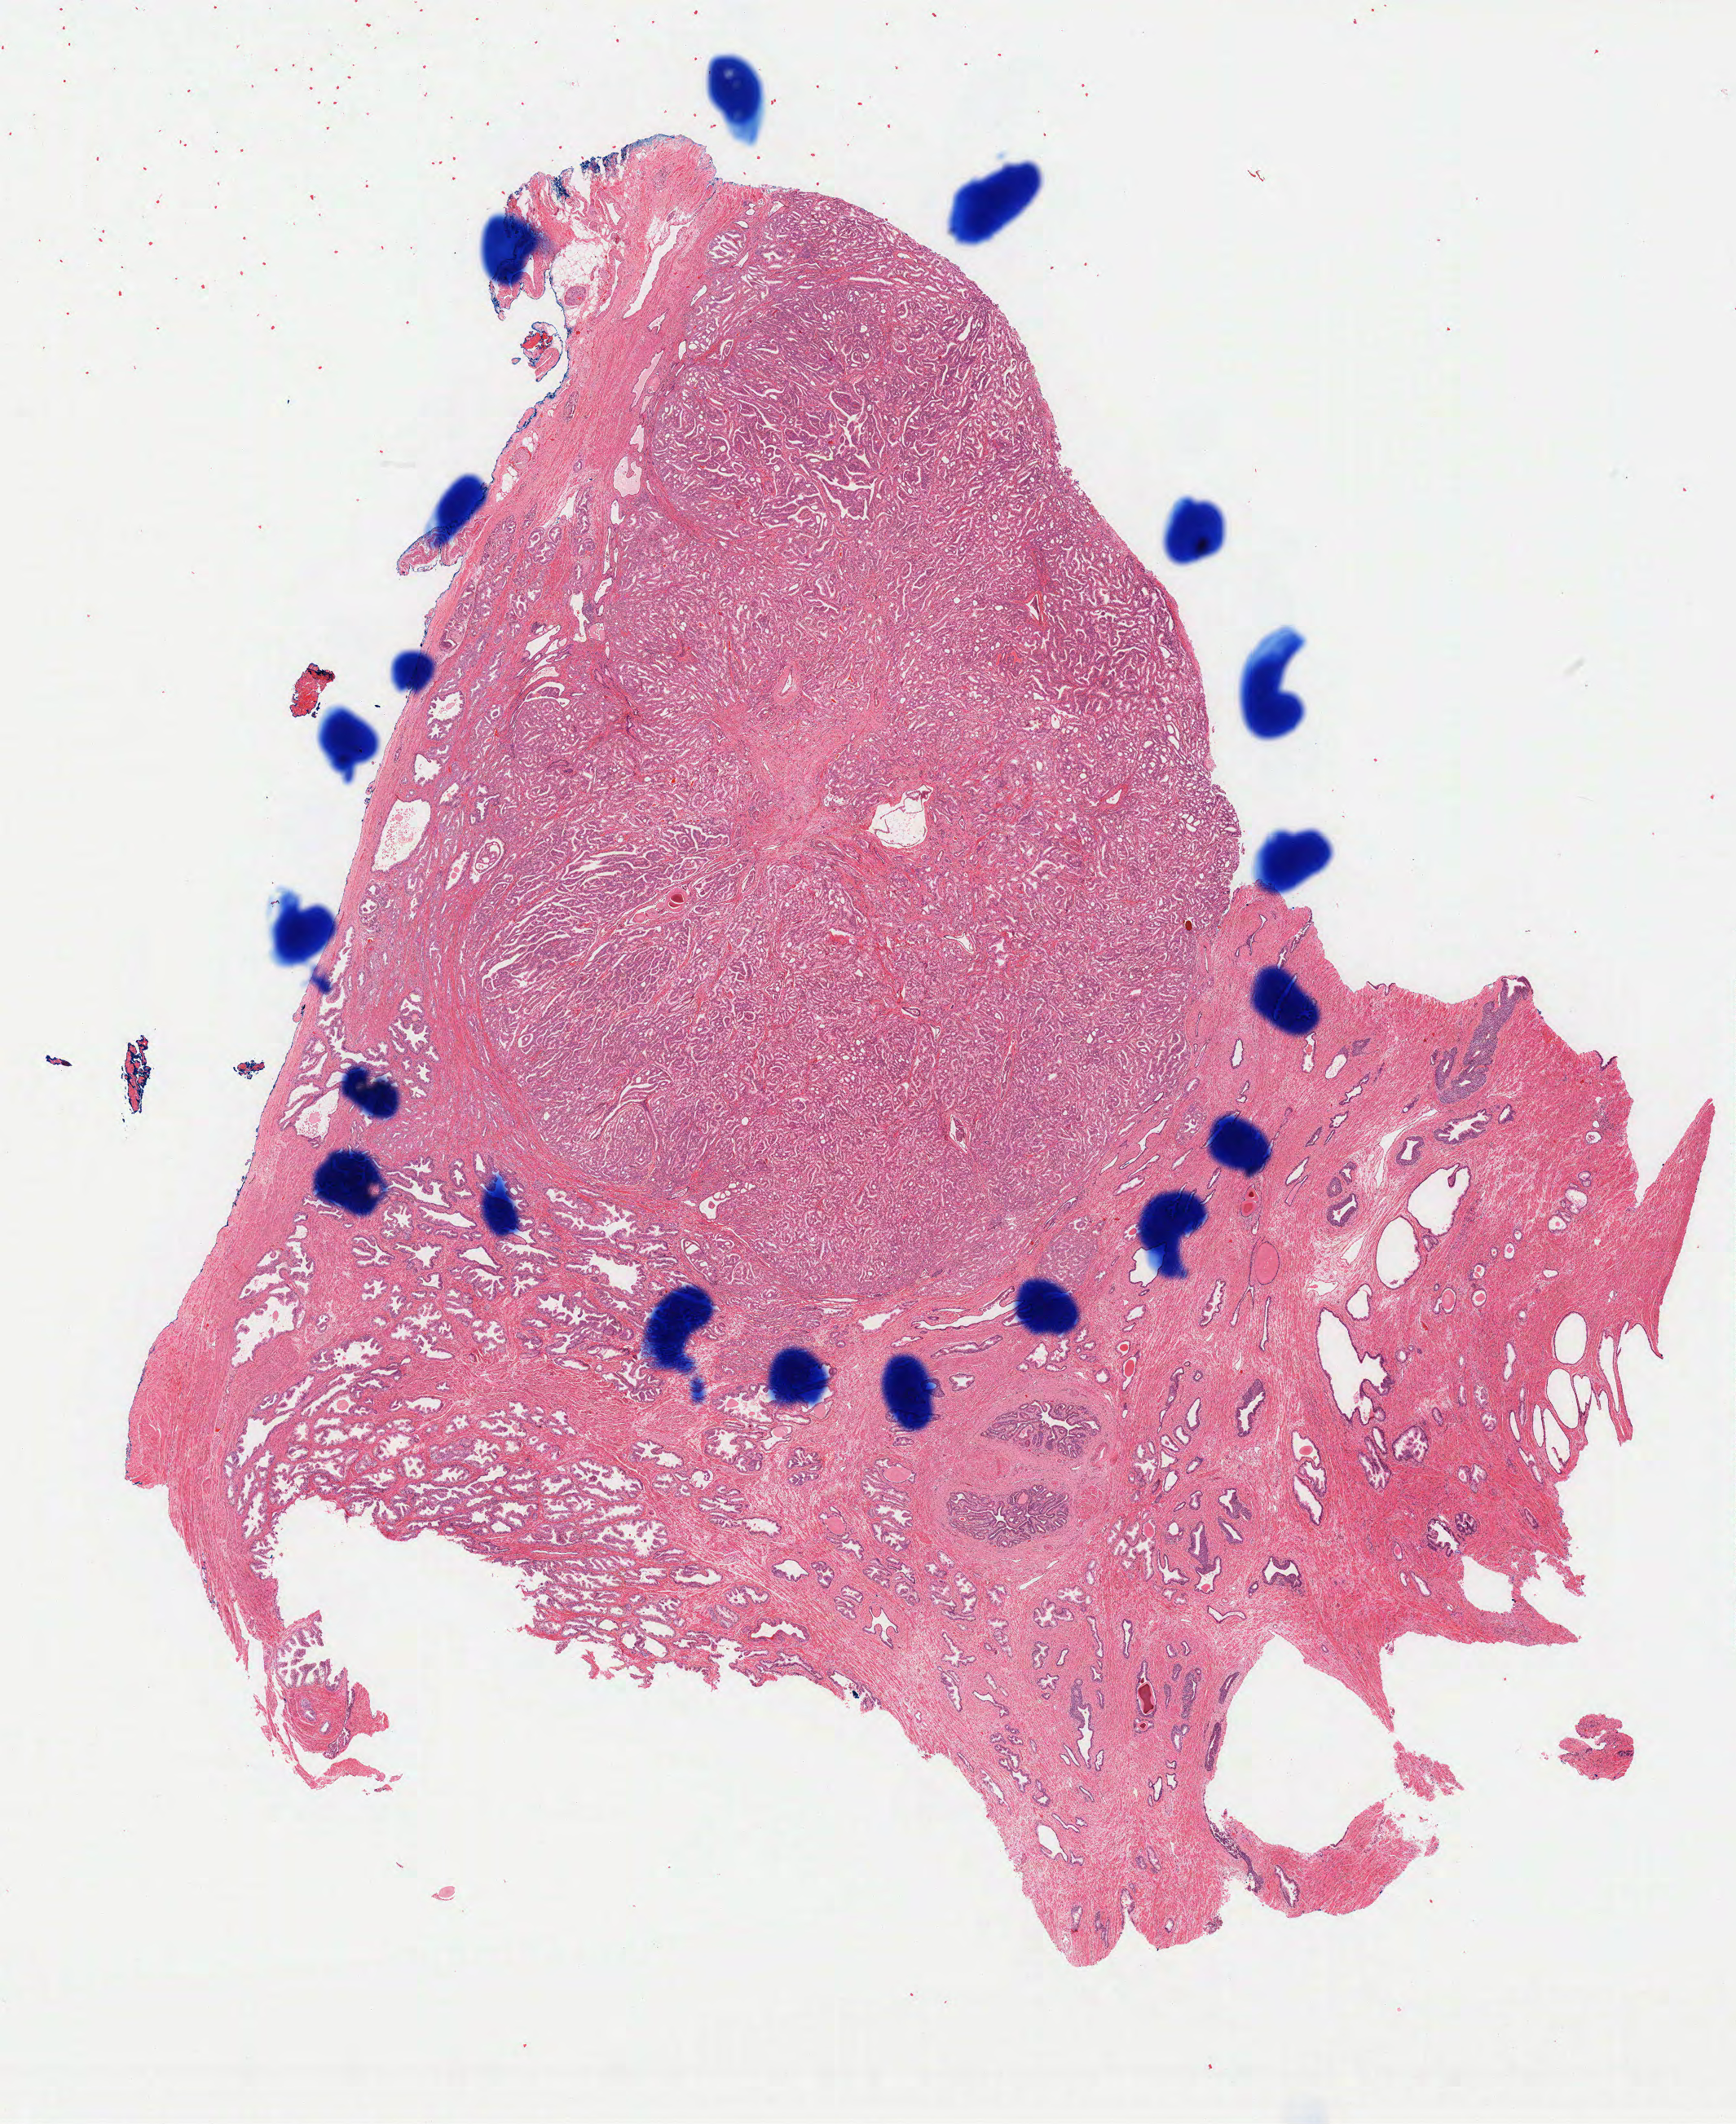
Hematoxylin and eosin (H&E) stained whole-slide image, a low-resolution overview of the entire scanned area, about 17.0 x 20.9 mm (slide scanned at 40x); FFPE section; sample: primary tumour, prostate. Male, age 63 years at initial diagnosis. Gleason score: 8 (4+4).
Histologic diagnosis: Adenocarcinoma, NOS (prostate gland). Lymph nodes positive (case pathology): 0 of 2 examined.